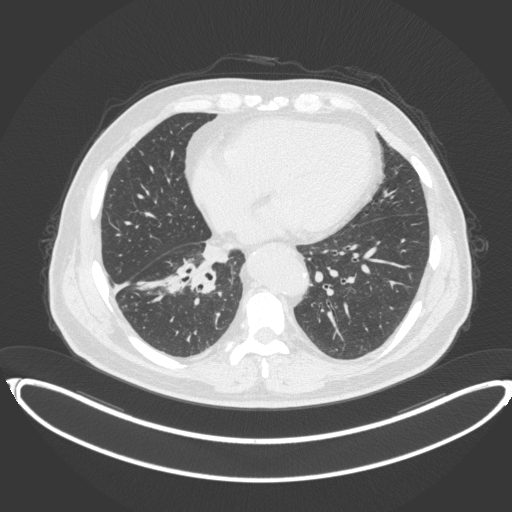
Chest CT, one axial slice. Slice 154 of 383 in the series (ordered by position). Reconstruction kernel B31f. Lung window (W 1500 / L -600 HU). 512 × 512 image matrix. Patient: male, 61 years. From the clinical record (not read from this slice): clinical TNM (as recorded): T1b N1 M0.
Annotated regions visible in this slice (rectangle marked by the reading radiologist):
- lung tumour (recorded histology: squamous cell carcinoma): box from (x=161, y=258) to (x=220, y=298) px